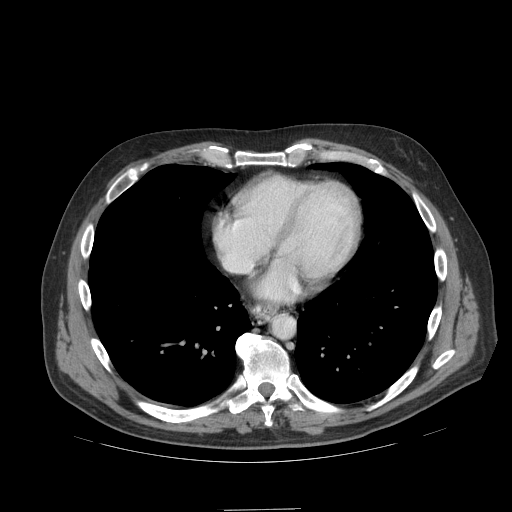
Contrast-enhanced abdominal CT (liver protocol), one axial slice. Position 99 of 99 along the scan axis. Reconstruction kernel STANDARD. 140 kVp. Soft-tissue window (W 400 / L 40 HU). 2.5 mm slice thickness. 512 × 512 image matrix, field of view 440 × 440 mm. From the clinical record (not read from this slice): diagnosis: hepatocellular carcinoma (patient treated with transarterial chemoembolisation; whether this scan precedes or follows treatment is not stated here); TNM stage (as recorded): Stage-I; Child-Pugh class: A; tumour nodularity: uninodular.
Structures marked on this image (semi-automatically segmented with operator editing):
- abdominal aorta: box from (x=273, y=315) to (x=294, y=338) px